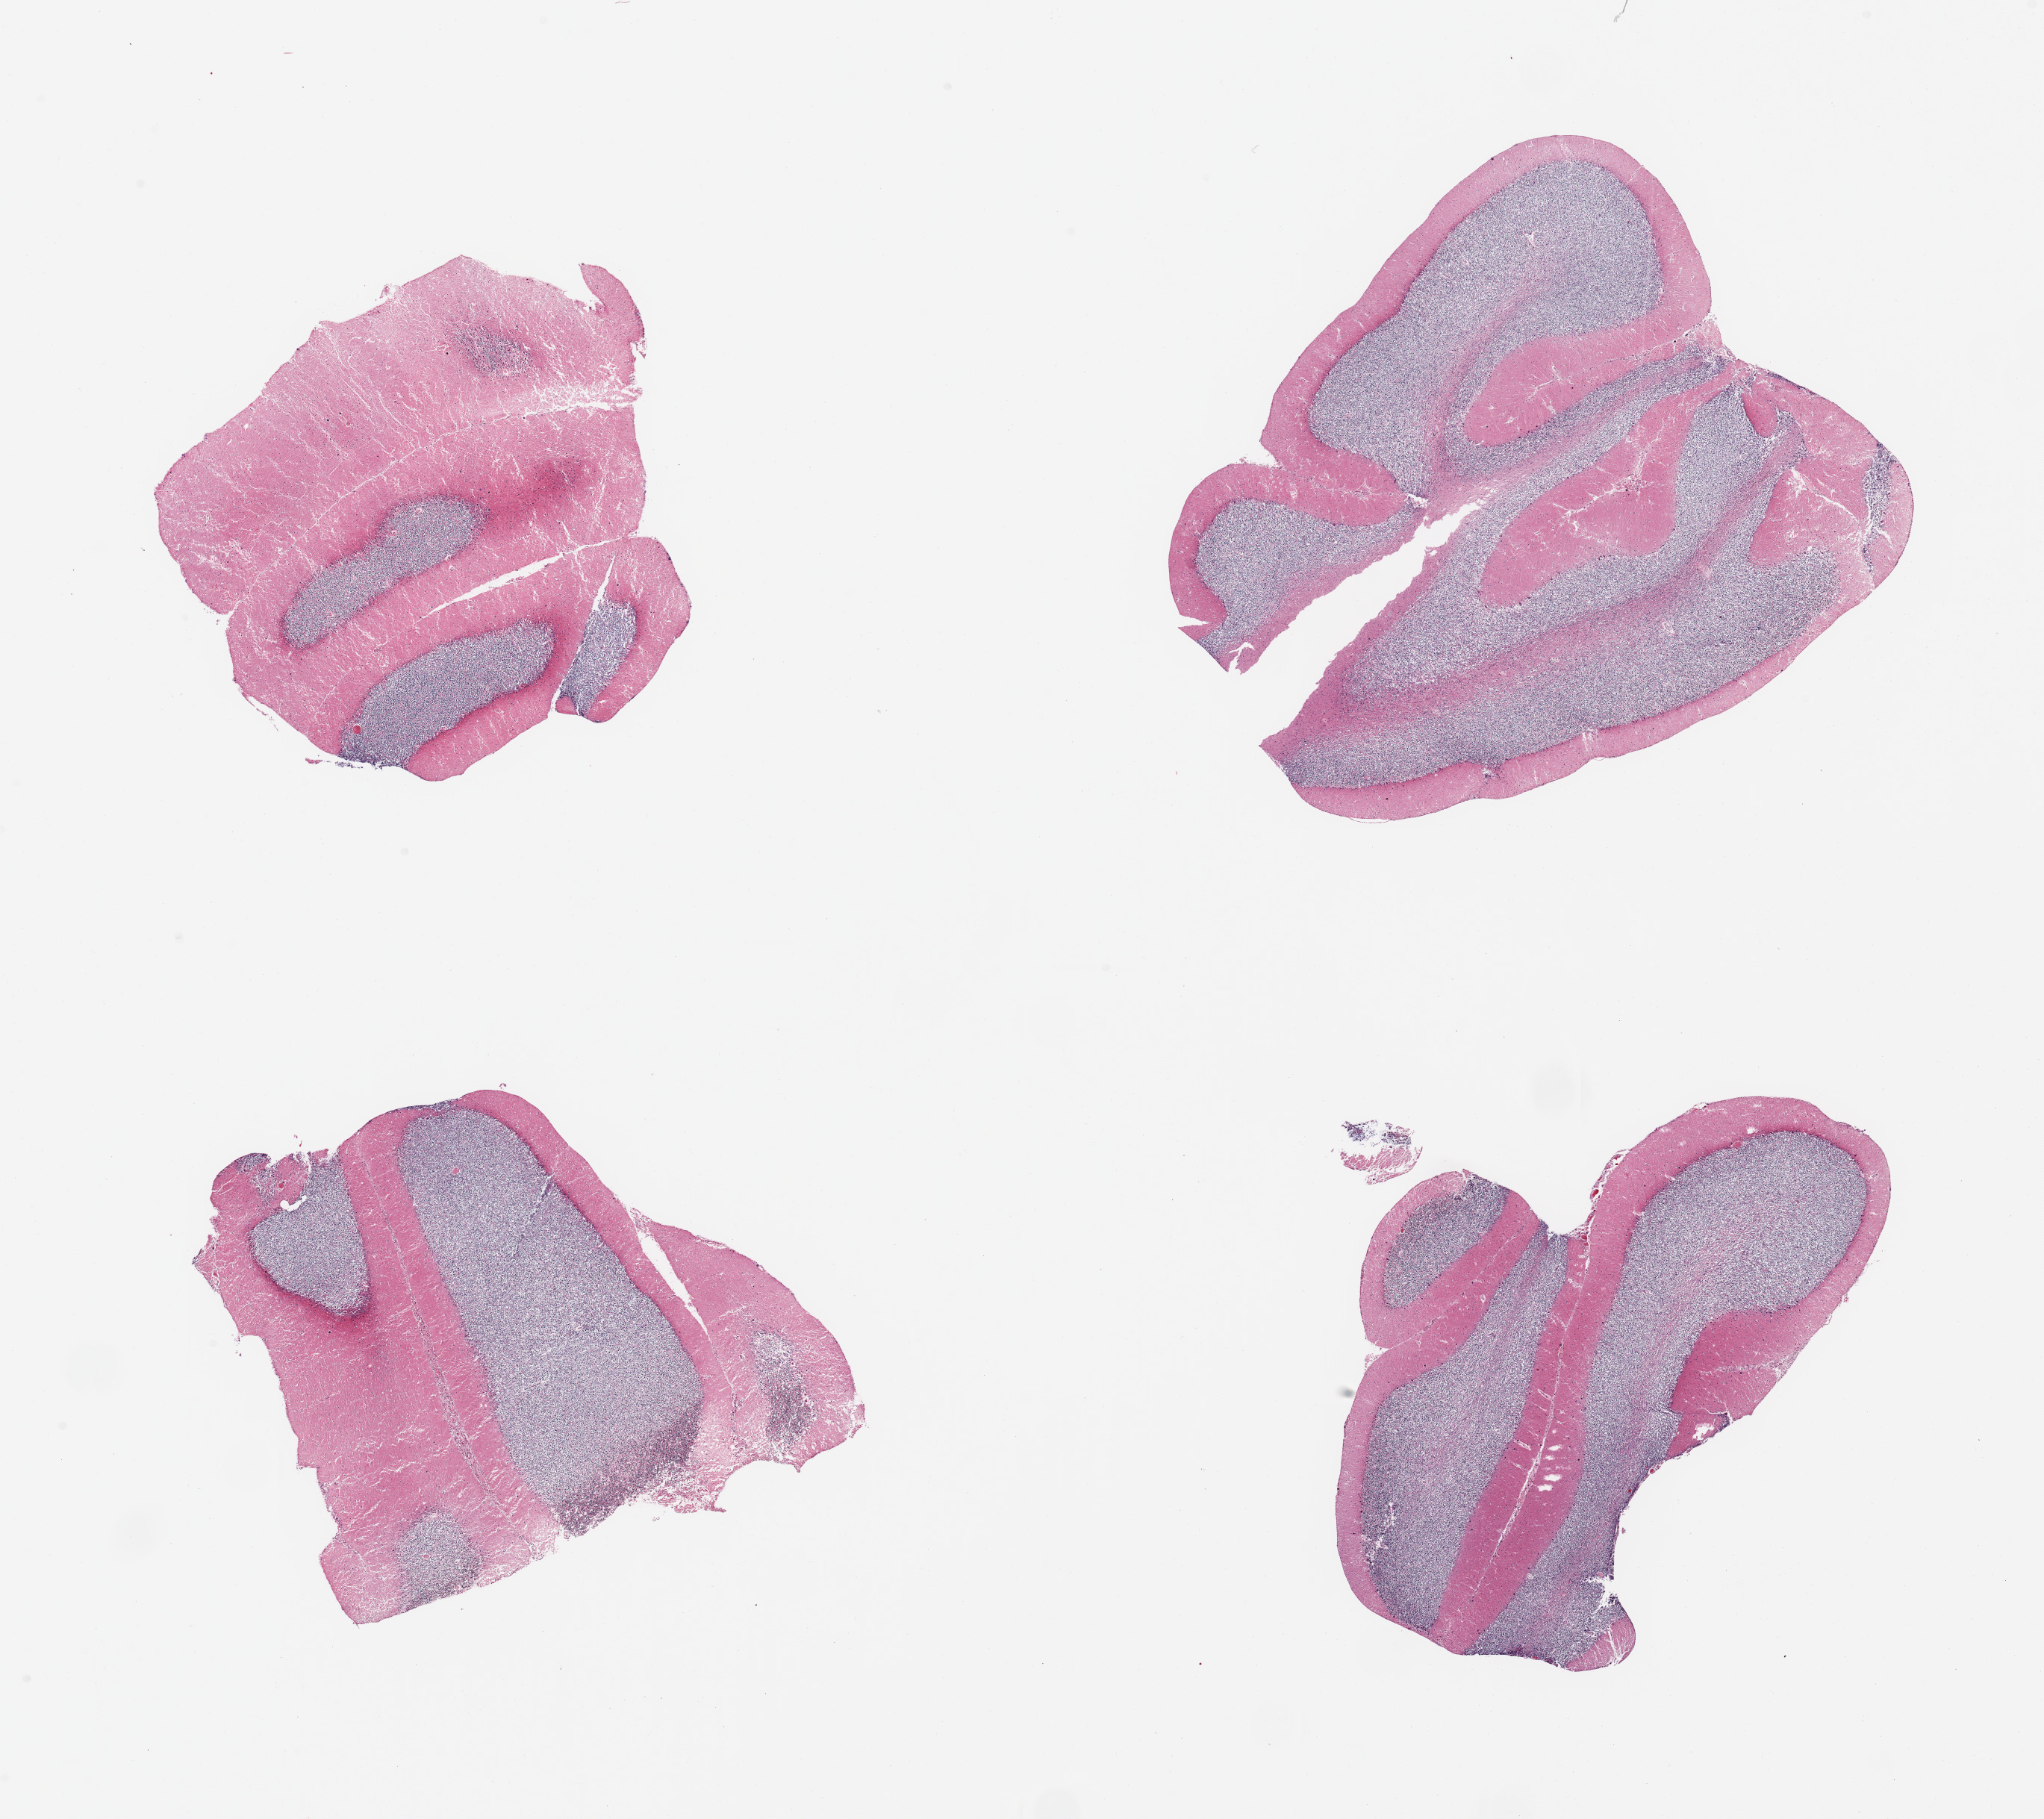
Whole-slide image, haematoxylin and eosin stain, brightfield, whole scanned area (about 21.7 x 19.3 mm, acquisition: 20x scan) shown as a low-resolution overview; PAXgene-fixed paraffin-embedded (PFPE) section; sampled site (target tissue): cerebellum; donor tissue sample.
Review note (as recorded): 4 pieces.